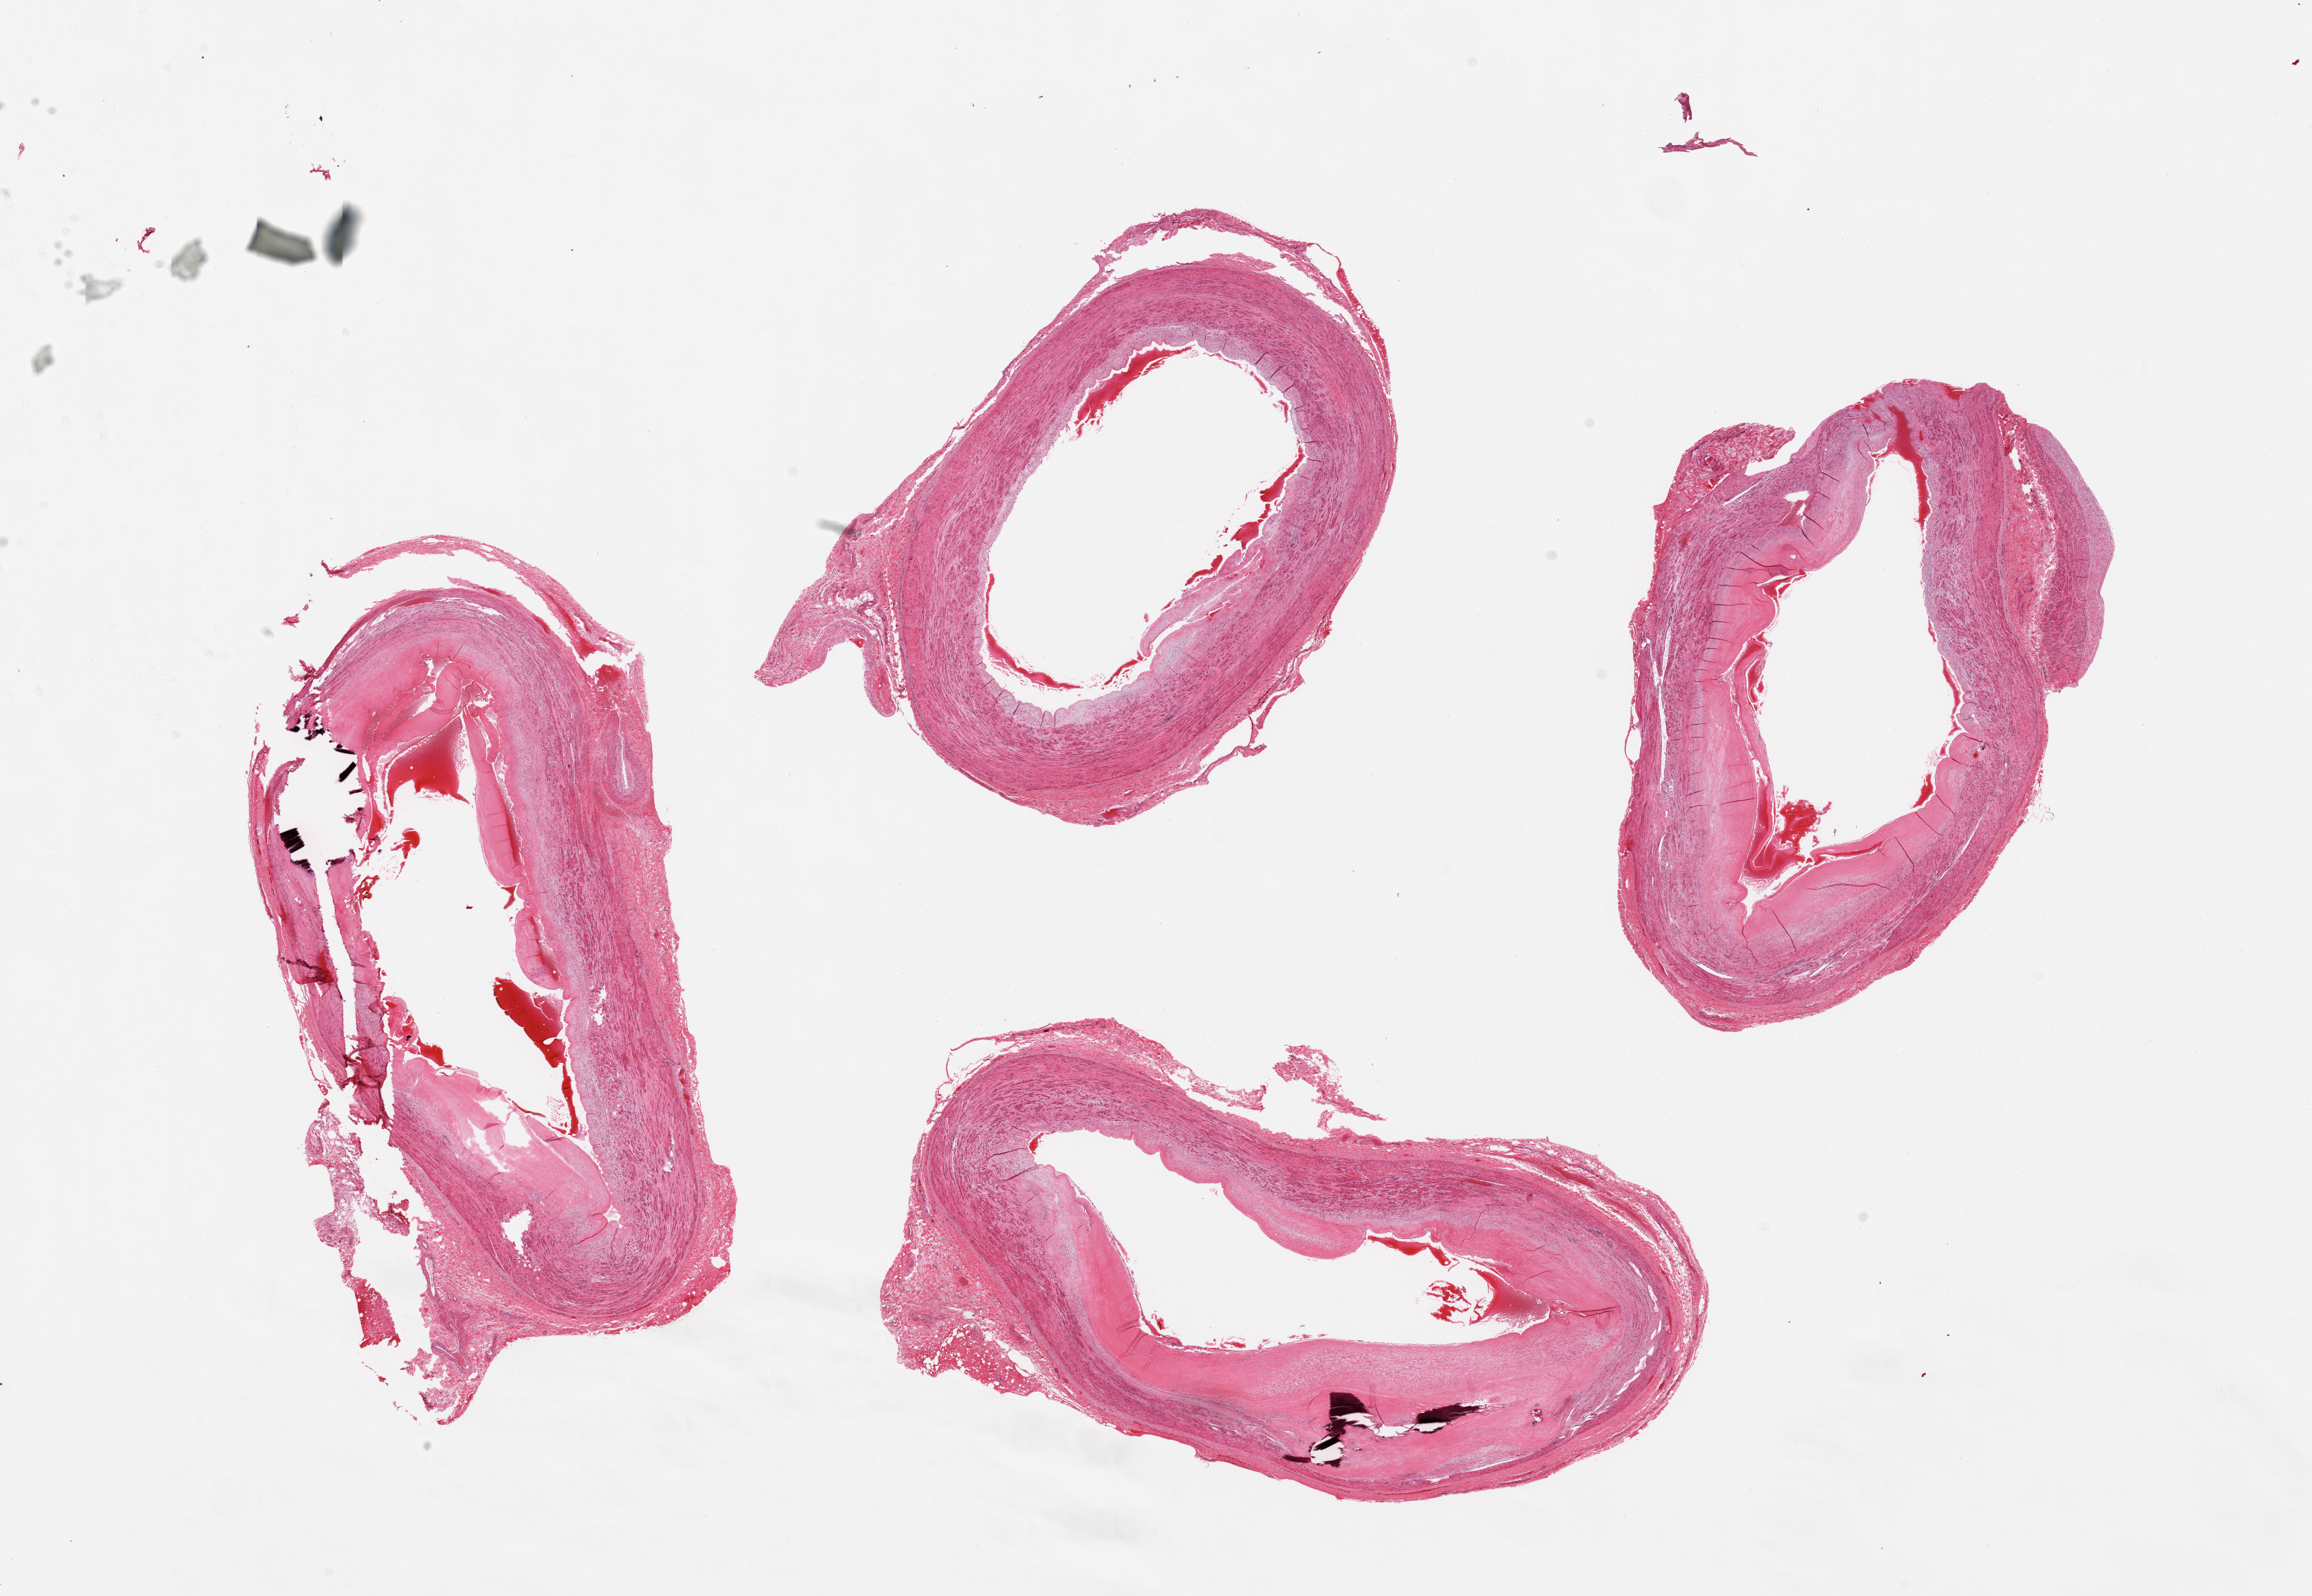
Whole-slide image, H&E stain, low-resolution overview of the scanned area, about 26.6 x 18.3 mm (slide scanned at 20x). PAXgene-fixed paraffin-embedded (PFPE) section. Section of tibial artery (target tissue). Tissue donor sample.
* reviewer comment on this tissue sample: 4 pieces, atherosclerotic changes with calcification compromising lumen